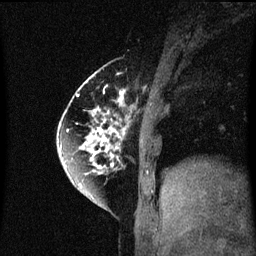
Breast MRI (dynamic contrast-enhanced), one sagittal slice. Position 17 of 60 along the scan axis. Dynamic contrast-enhanced series, image 2 of 3 at this slice position (ordered by acquisition). 1.5 T. TE 4.2 ms, TR 8.4 ms. 2 mm slice thickness. 256 × 256 image matrix, field of view 200 × 200 mm. Female patient, age 60 years.
Annotated regions visible in this slice (semi-automatically segmented with operator editing):
- analysis volume of interest (the breast-tissue region the enhancement analysis was run in; not a lesion): box from (x=64, y=70) to (x=131, y=195) px
- tumour enhancement mask (voxels above the 70 % enhancement threshold inside the analysis volume of interest): (x=64, y=72)–(x=127, y=177)